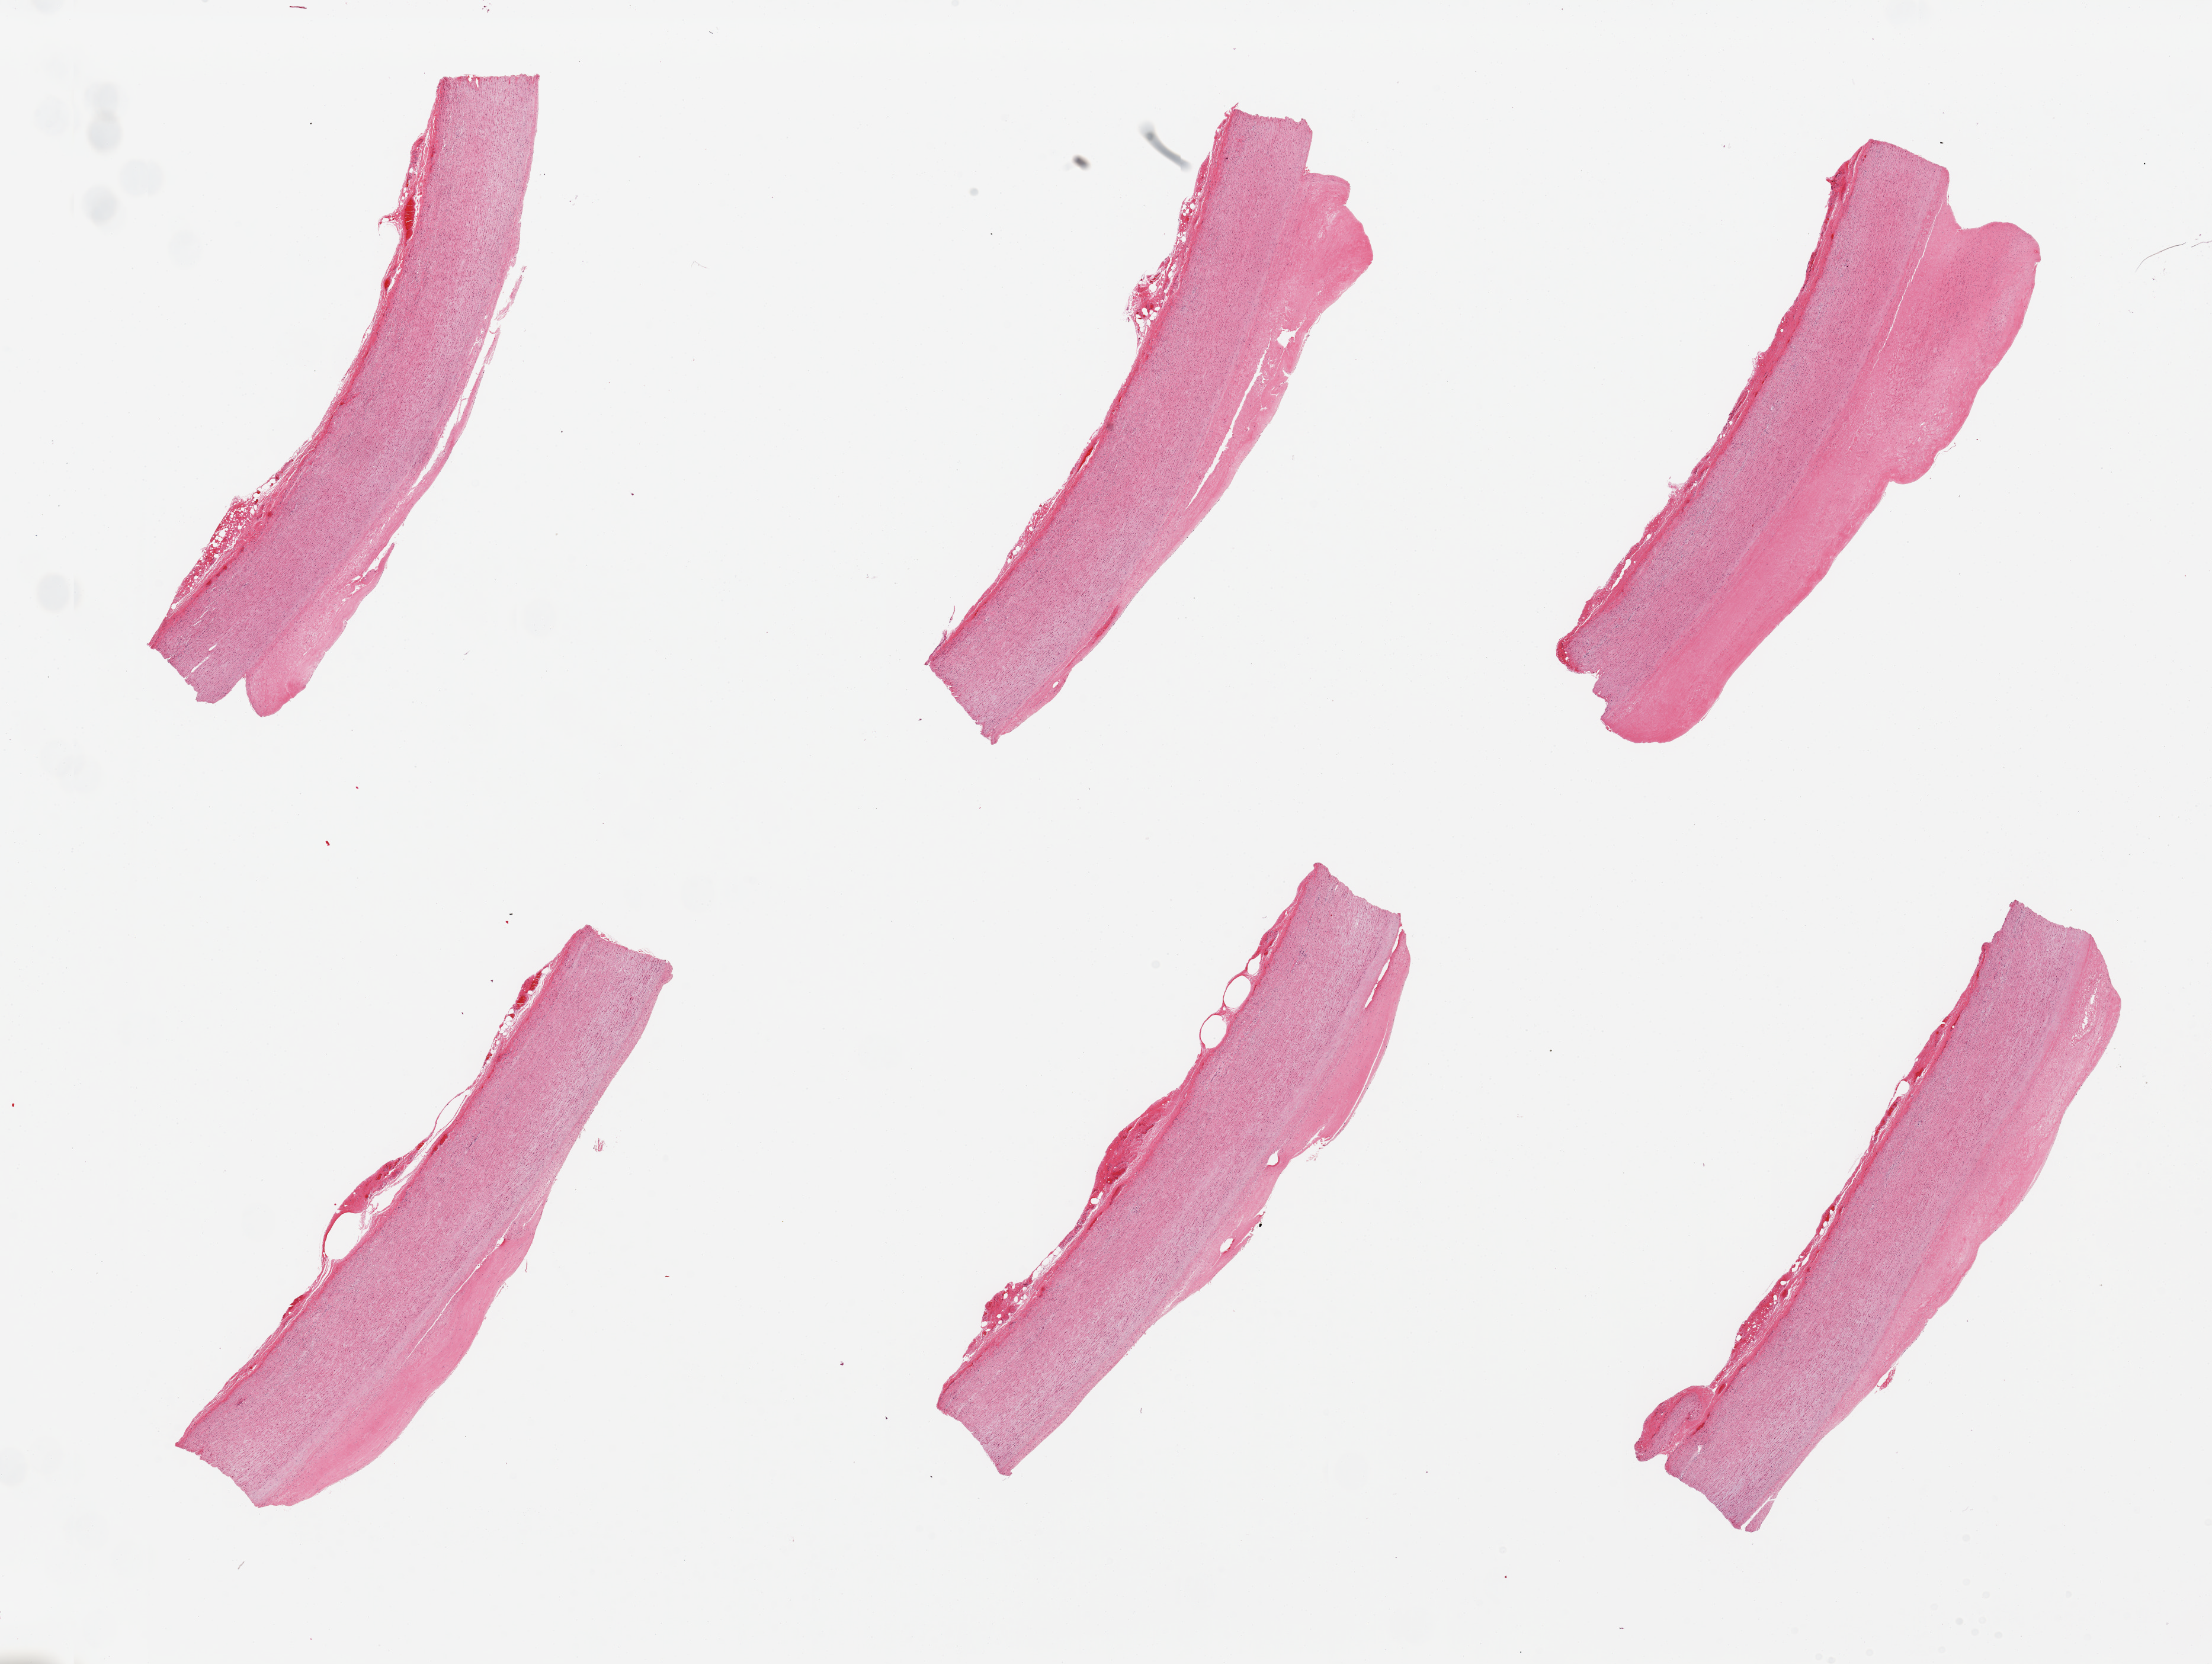
Whole-slide image, H&E stain, low-resolution overview of the scanned area, about 29.5 x 22.2 mm. PAXgene-fixed paraffin-embedded (PFPE) section. Sampled site (target tissue): aorta. Tissue donor sample. Donor: female.
Pathologist's review note for this sample: 6 pieces, prominent atherosis.